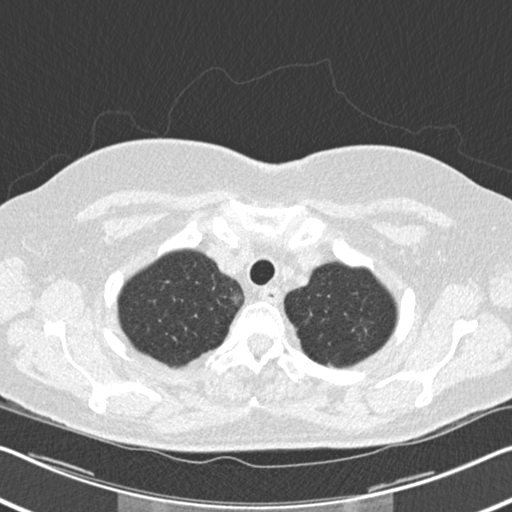
Axial slice from a low-dose chest CT screening exam; second annual screen; lung window (W 1500 / L -600 HU); standard (soft-tissue) reconstruction kernel (B30f); 120 kVp; slice 31 of 202 in the series; 512 × 512 image matrix, field of view 336 × 336 mm. Female participant, aged 60 years at enrolment. Current smoker at enrolment.
Lesion marked by an expert reader, bounding box (x1, y1, x2, y2) in pixels: (333, 313, 378, 354). The screening reader recorded 6 non-calcified nodules or masses ≥4 mm on this exam; which of them this box marks is not recorded. Later outcome: lung cancer diagnosed 495 days after this screen — non-small cell carcinoma, left upper lobe, poorly differentiated (G3), stage IB (AJCC 6th edition), 7 mm at pathology.